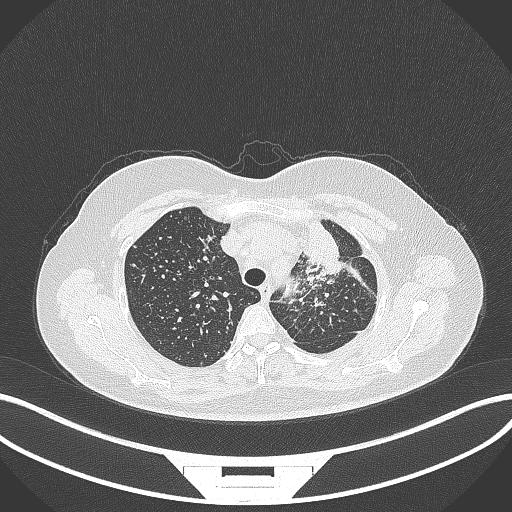
Chest CT, one axial slice. Position 263 of 348 along the scan axis. Reconstruction kernel B70f. Lung window (W 1500 / L -600 HU). 1 mm slice thickness. 512 × 512 image matrix, field of view 400 × 400 mm. Female patient, age 49 years. From the clinical record (not read from this slice): clinical TNM (as recorded): T1c N0 M1.
Outlined on this slice (rectangle marked by the reading radiologist):
- lung tumour (recorded histology: adenocarcinoma): bounding box (x1, y1, x2, y2) in pixels: (298, 215, 348, 275)